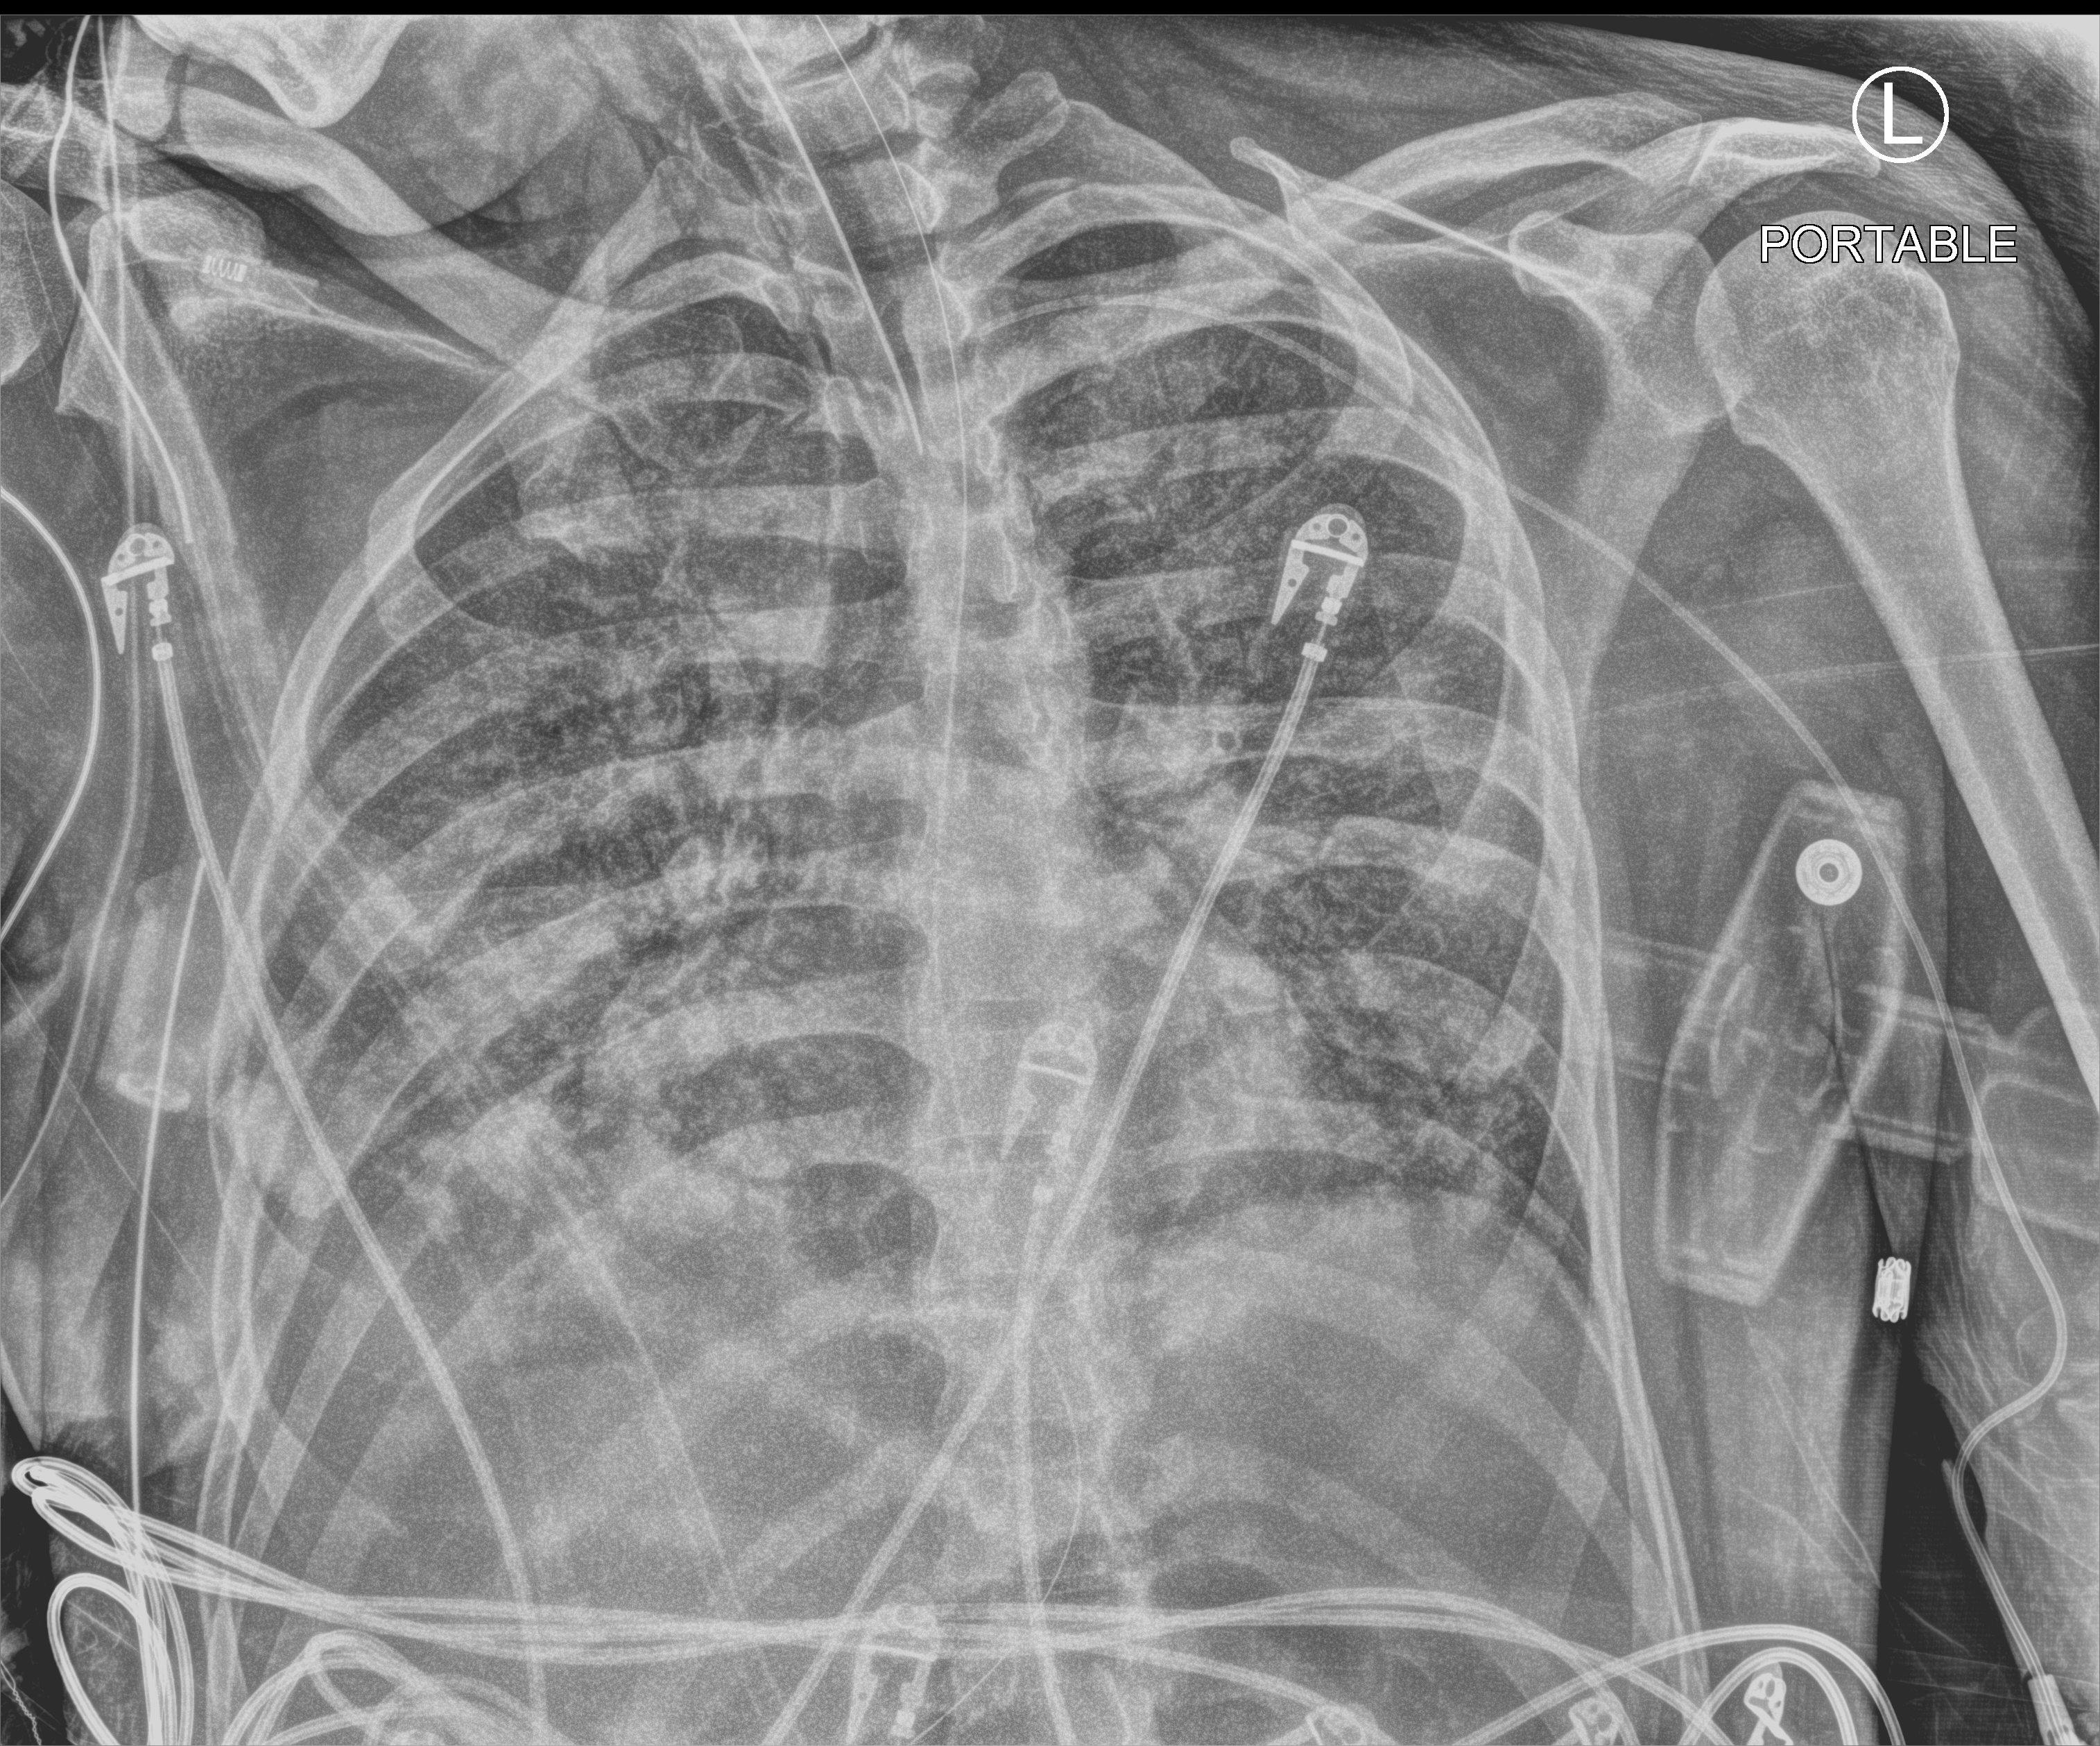
Portable chest radiograph; anteroposterior (AP) projection. Male patient hospitalised with COVID-19, age 18–59 years.
Hospital-stay facts (about this admission, not read from this image; timing relative to this image not recorded):
- mechanically ventilated during this hospital stay: yes